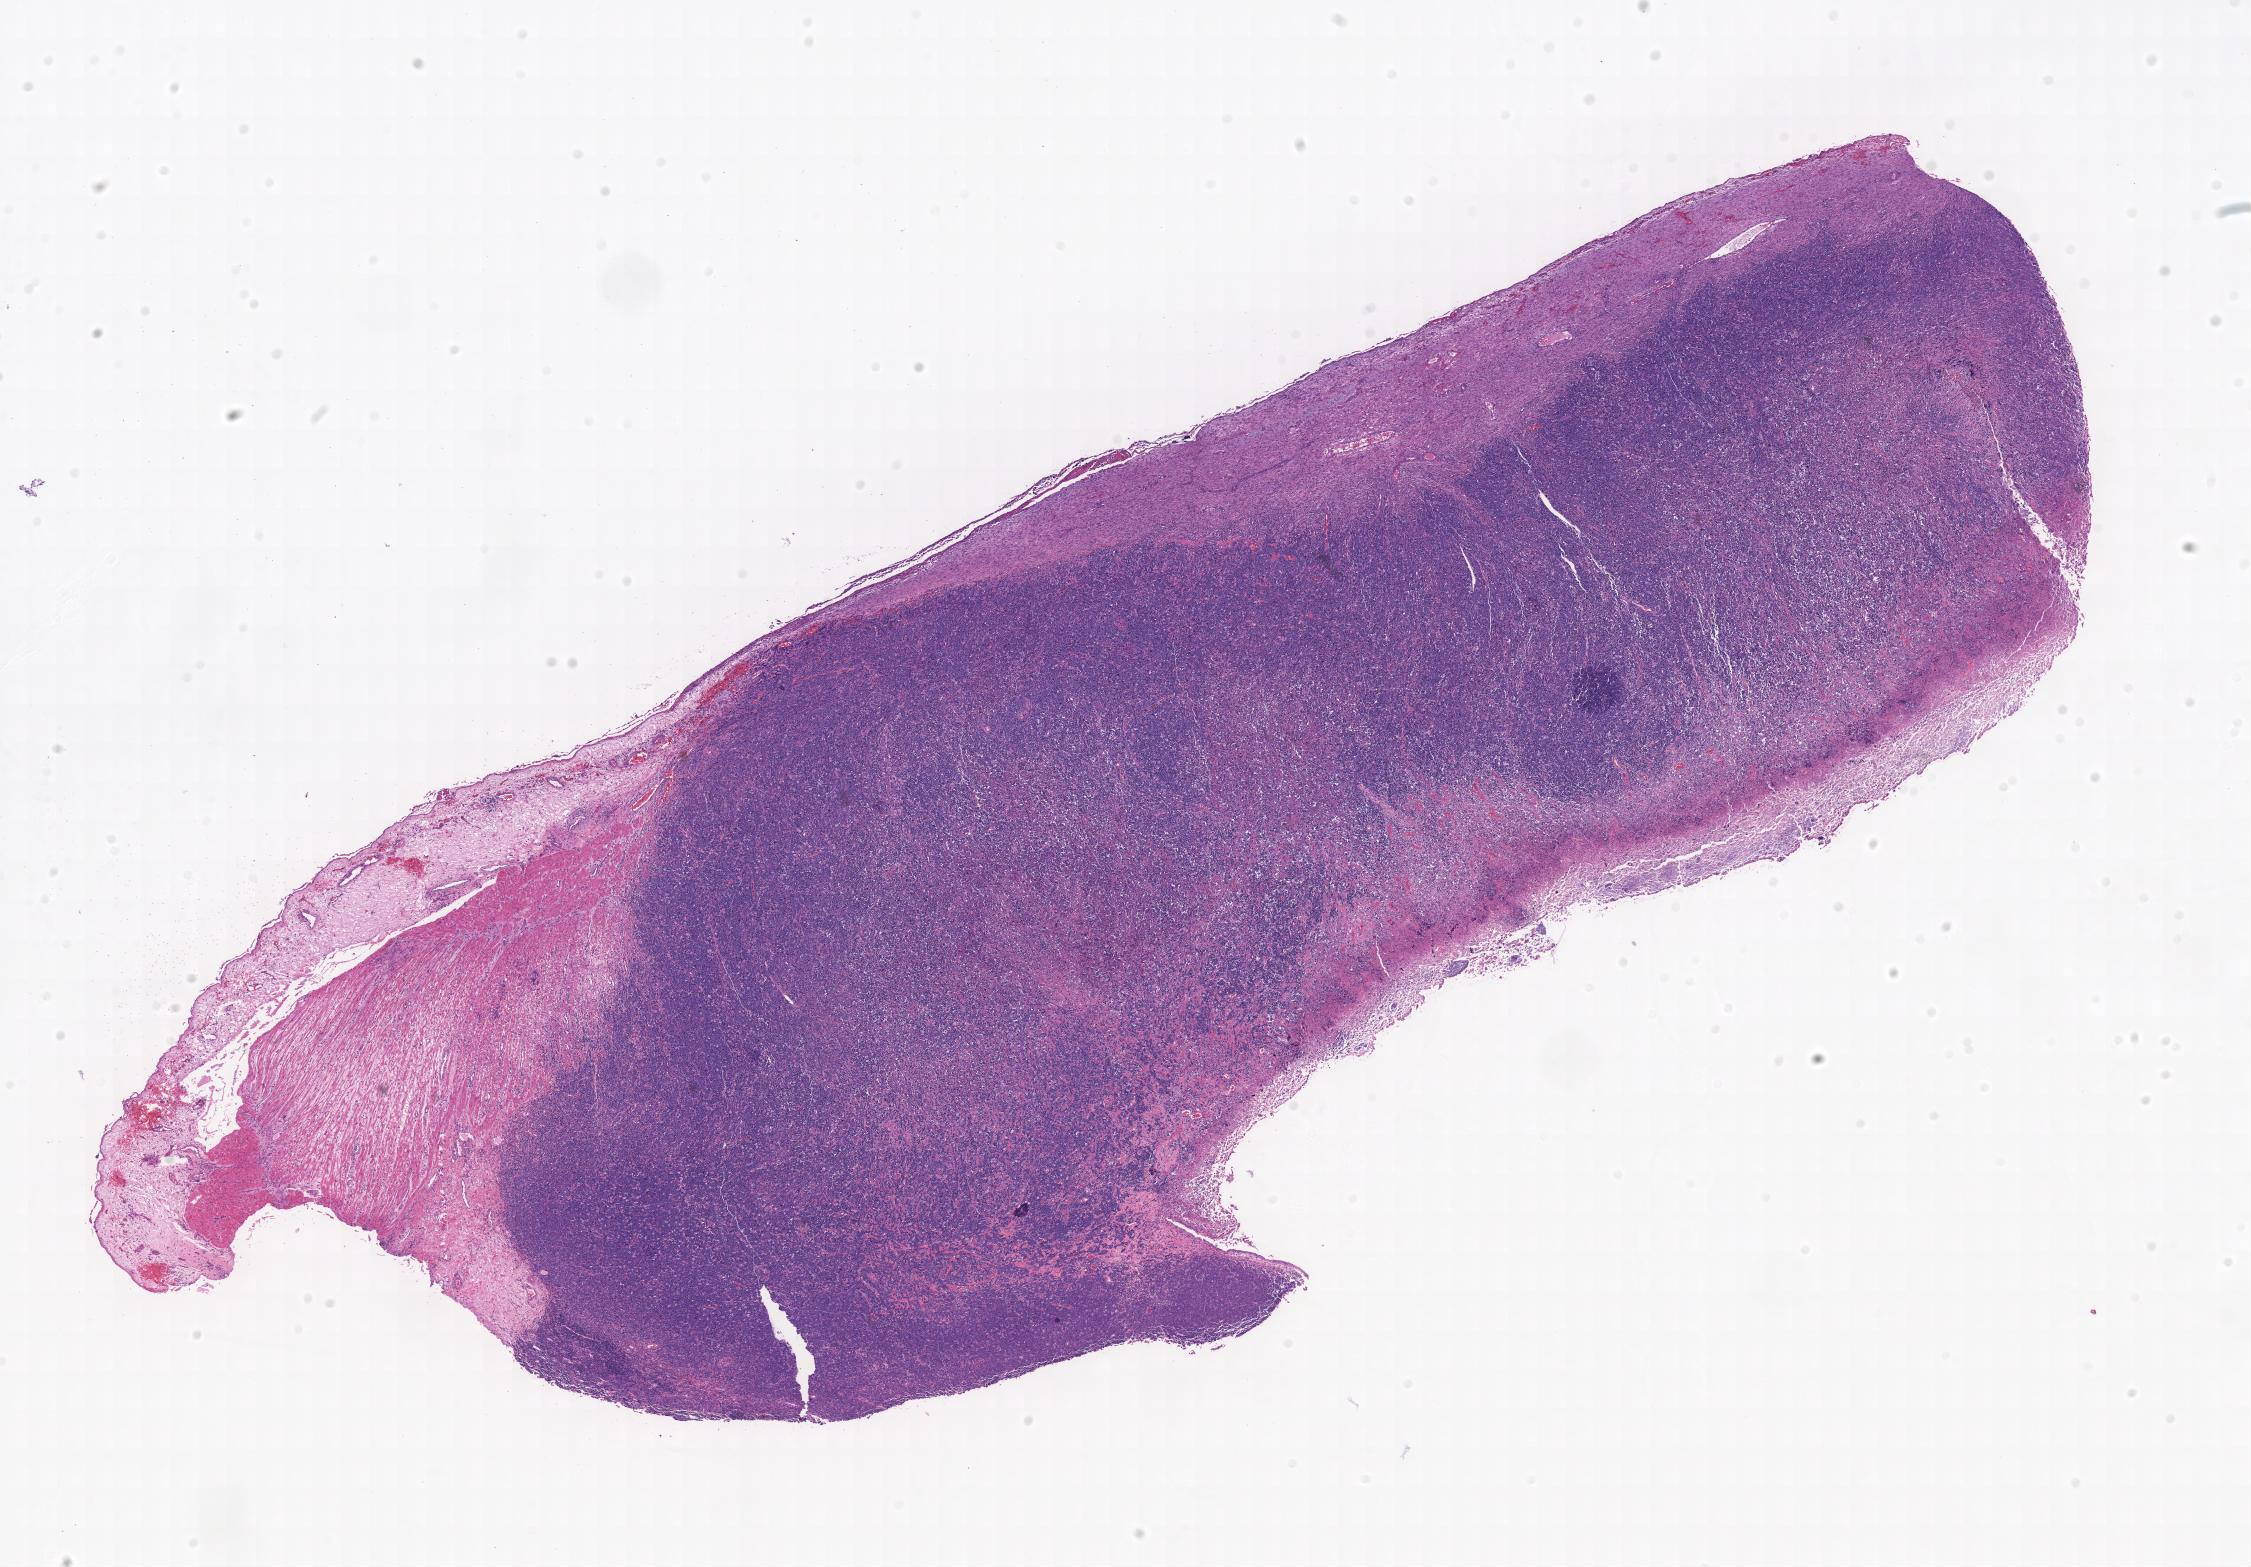
Digitized haematoxylin and eosin-stained section — whole scanned area shown as a low-resolution overview, tumor tissue, site: small intestine. Male patient; age at initial diagnosis 3 years.
Diagnosis: Burkitt lymphoma, NOS.